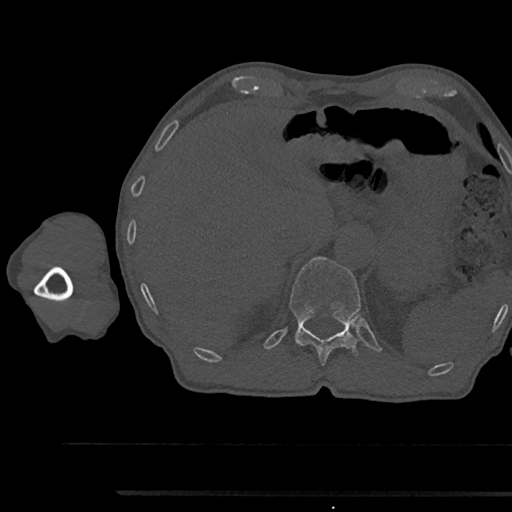
CT including the spine, one axial slice. Slice 712 of 797 in the series (ordered by position). Reconstruction kernel Br40s/3. Bone window (W 1800 / L 400 HU). 0.5 mm slice thickness. 512 × 512 image matrix, field of view 367 × 367 mm. Patient: male, 79 years. From the clinical record (not read from this slice): primary cancer: prostate.
Structures marked on this image (semi-automatic segmentation, software-assisted and operator-edited):
- T12 vertebra: bounding box <289,257,362,366> (left, top, right, bottom; pixels)